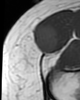
MRI of an extremity soft-tissue mass, one axial slice. Position 15 of 46 along the scan axis. MR volume resampled by the dataset authors to the PET/CT grid (not the native acquisition matrix). 3.27 mm slice thickness. 80 × 100 image matrix, field of view 78 × 98 mm. Female patient. From the clinical record (not read from this slice): histological type: synovial sarcoma; grade: intermediate; site of the primary tumour: right thigh.
Outlined on this slice (expert contour drawn on MRI and transferred to this co-registered scan by the dataset authors):
- gross tumour volume including surrounding oedema: bounding box <32,24,58,54> (left, top, right, bottom; pixels)
- gross tumour volume (mass): <32,24,58,54>